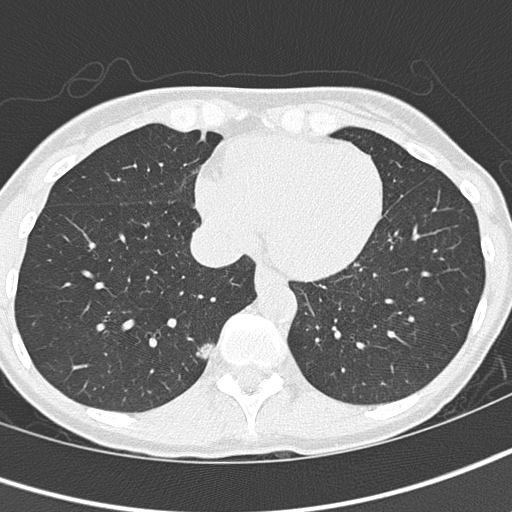
Axial slice from a low-dose chest CT screening exam, baseline screening round, lung window (W 1500 / L -600 HU), 512 × 512 image matrix, field of view 276 × 276 mm. Female, age 57 years at enrolment. Current smoker at enrolment.
Expert reader's lesion annotation, box from (x=183, y=337) to (x=220, y=366) px. Screening reader's record for this exam (one nodule recorded; not confirmed to be the boxed lesion): non-calcified nodule or mass ≥4 mm, right lower lobe, 11 × 6 mm, mixed attenuation. Official screen result: positive, change unspecified: nodule(s) >= 4 mm or enlarging nodule(s), mass(es), or other non-specific abnormalities suspicious for lung cancer. Lung cancer was diagnosed 61 days after this screen: adenocarcinoma, NOS, right lower lobe, moderately differentiated (G2), stage IA (AJCC 6th edition), 8 mm at pathology.